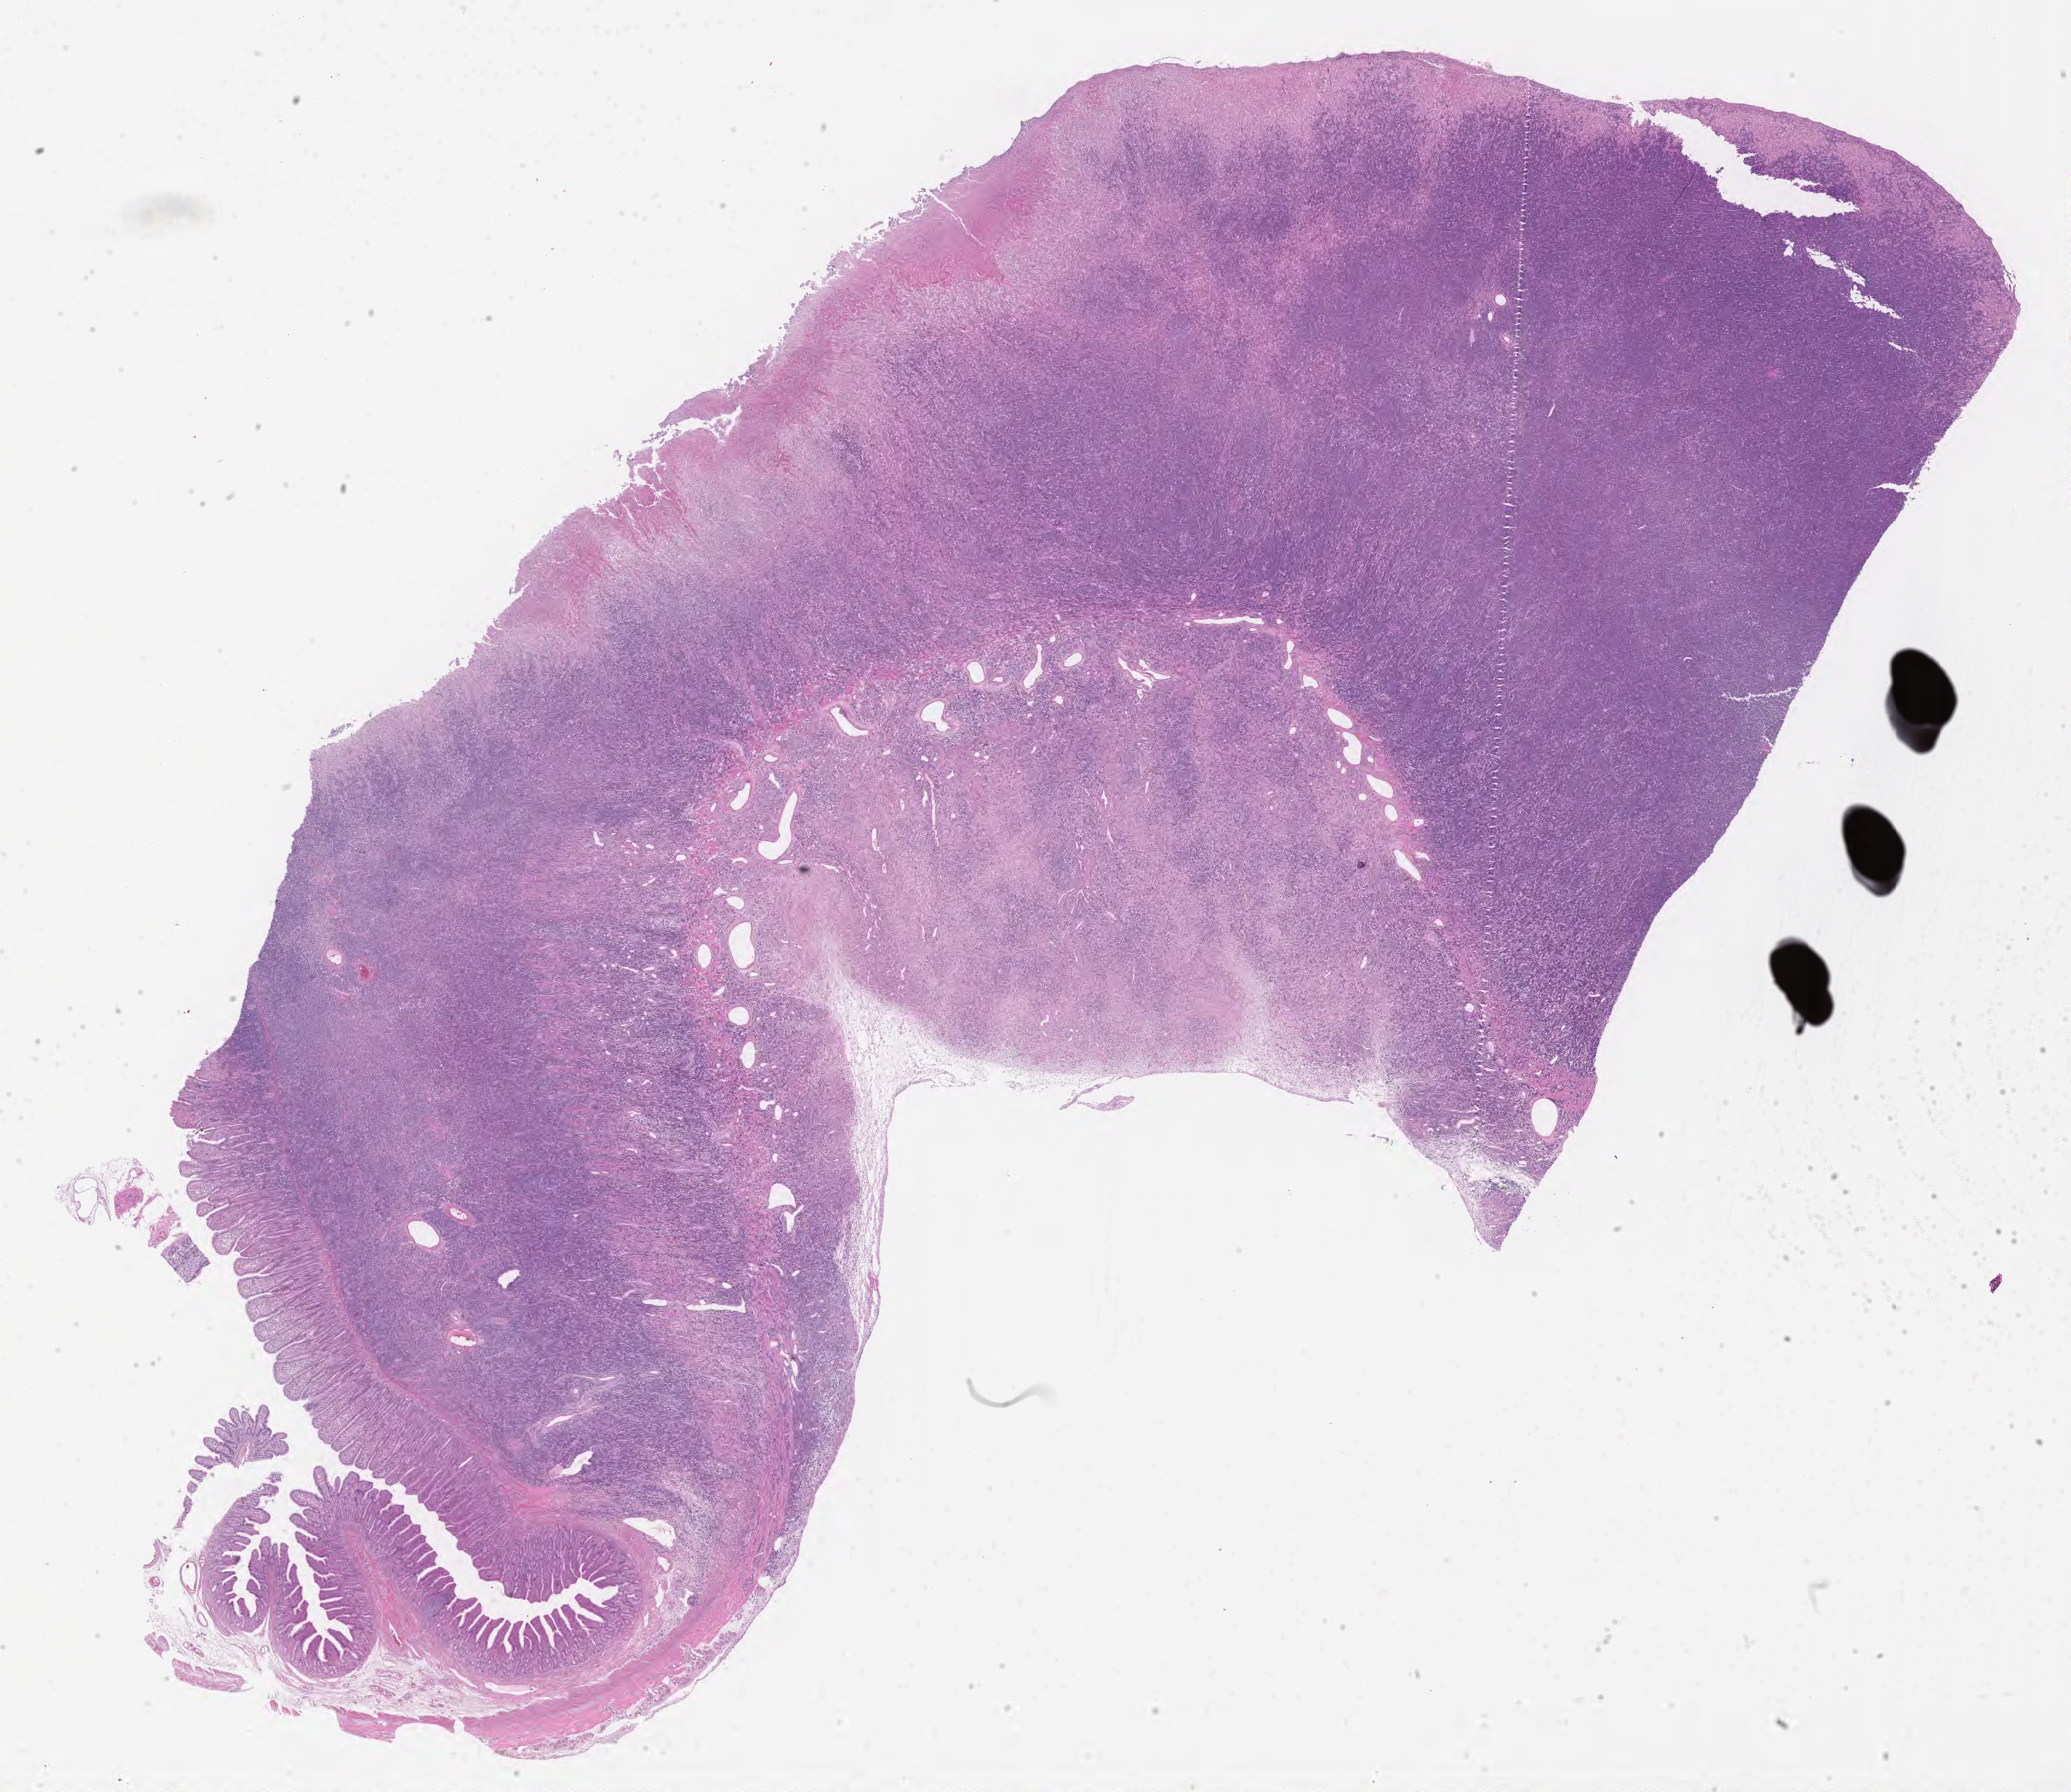
Digitized haematoxylin and eosin-stained section, whole scanned area (about 23.6 x 20.5 mm) shown as a low-resolution overview. Specimen: tumor tissue. Male patient; age at initial diagnosis 4 years.
Diagnosis: Burkitt lymphoma, NOS.